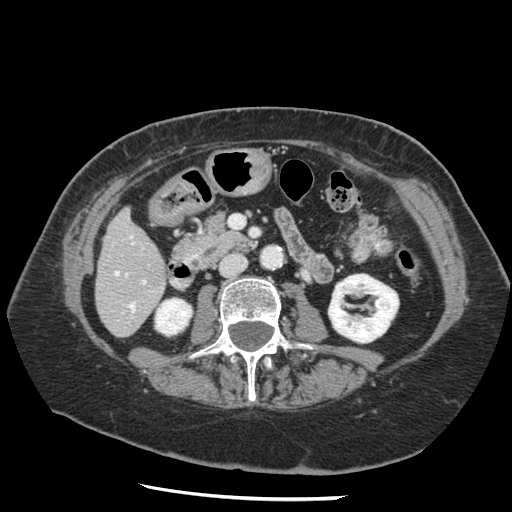
Contrast-enhanced abdominal CT, one axial slice. Position 43 of 148 along the scan axis. 120 kVp. Intravenous contrast given. Soft-tissue window (W 400 / L 40 HU). 2.5 mm slice thickness. 512 × 512 image matrix, field of view 330 × 330 mm. Female patient, age 85 years. Case-level facts recorded for this patient, not image findings: diagnosis: colorectal cancer liver metastases, imaged before liver resection; multiple liver metastases: no; largest metastasis: 0.9 cm; disease in both lobes: no.
Structures marked on this image (outlined manually by an expert reader):
- hepatic veins: box from (x=115, y=271) to (x=134, y=312) px
- liver: (x=96, y=210)–(x=166, y=336)
- planned liver remnant (the part of the liver to remain after resection): (x=96, y=210)–(x=166, y=333)